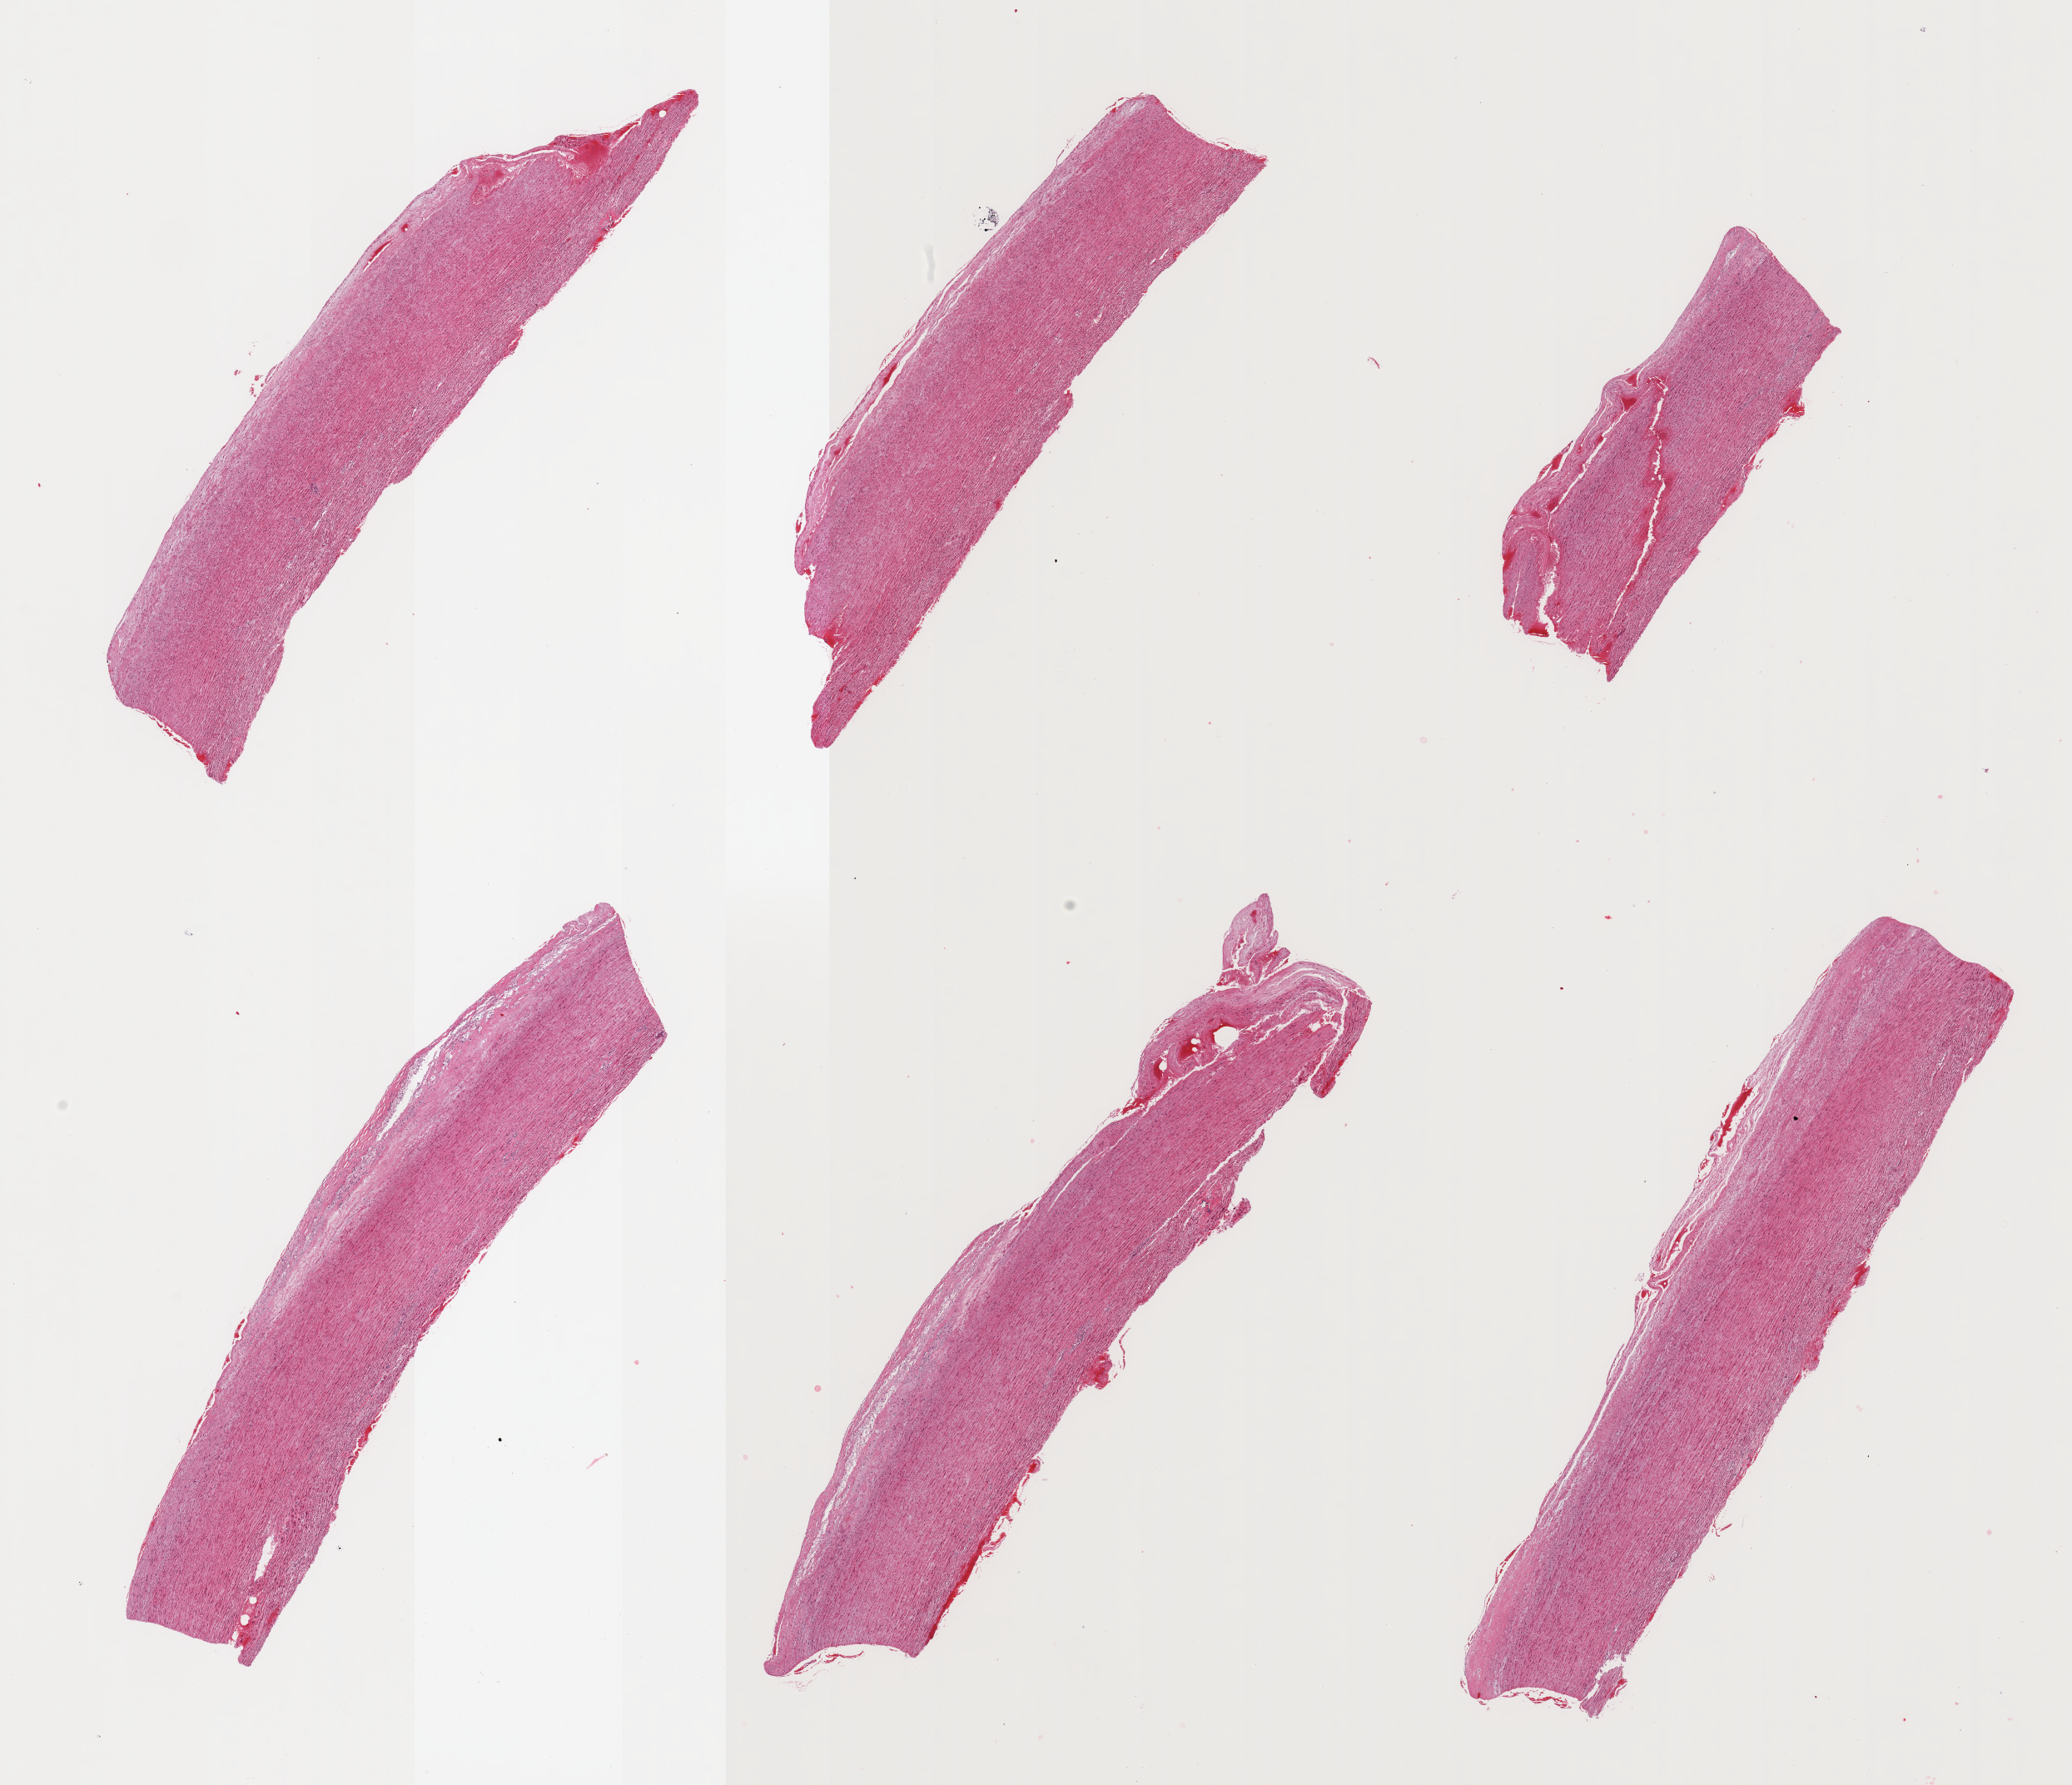
Haematoxylin and eosin whole-slide image — shown as a low-resolution overview of the whole scanned area (about 19.7 x 17.0 mm). PAXgene-fixed, paraffin-embedded tissue. Sampled site (target tissue): aorta. Donor tissue sample. Female donor.
Pathologist's review note for this sample: 6 pieces; 1 with a large diagonal fracture with recent hemorrhage; history of aortic dissection.